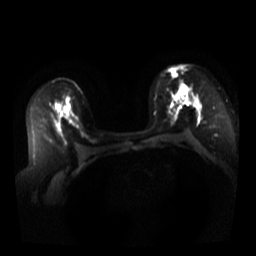
Breast MRI, one axial slice. Slice 22 of 44 in the series (ordered by position). Diffusion-weighted series; image 2 of 4 stored at this slice position (different b-values; order by instance number). 3 T. 256 × 256 image matrix, field of view 340 × 340 mm. Female patient.
Outlined on this slice (outlined manually by an expert reader):
- tumour on diffusion-weighted imaging: box from (x=173, y=72) to (x=187, y=93) px